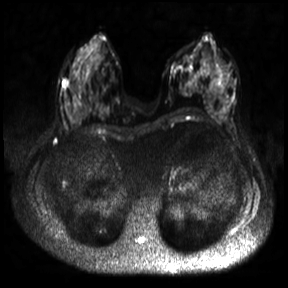
Breast MRI, one axial slice. Diffusion-weighted series; image 2 of 4 stored at this slice position (different b-values; order by instance number). 3 T. 4 mm slice thickness. 288 × 288 image matrix, field of view 360 × 360 mm. Female patient.
Annotated regions visible in this slice (expert manual segmentation):
- tumour on diffusion-weighted imaging: bounding box <63,80,69,87> (left, top, right, bottom; pixels)